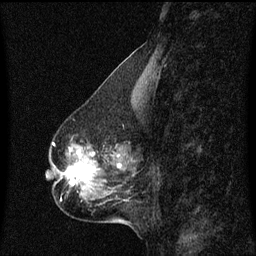
Breast MRI (dynamic contrast-enhanced), one sagittal slice; slice 24 of 60 in the series (ordered by position); dynamic contrast-enhanced series, image 2 of 3 at this slice position (ordered by acquisition); 1.5 T; TE 4.2 ms, TR 8.4 ms; 2 mm slice thickness; 256 × 256 image matrix. Female patient, age 50 years. From the clinical record (not read from this slice): setting: breast cancer imaged before/during neoadjuvant chemotherapy; receptor status: HR-positive, HER2-negative.
Outlined on this slice (semi-automatically segmented with operator editing):
- analysis volume of interest (the breast-tissue region the enhancement analysis was run in; not a lesion): box from (x=55, y=140) to (x=129, y=191) px
- tumour enhancement mask (voxels above the 70 % enhancement threshold inside the analysis volume of interest): (x=65, y=148)–(x=123, y=187)